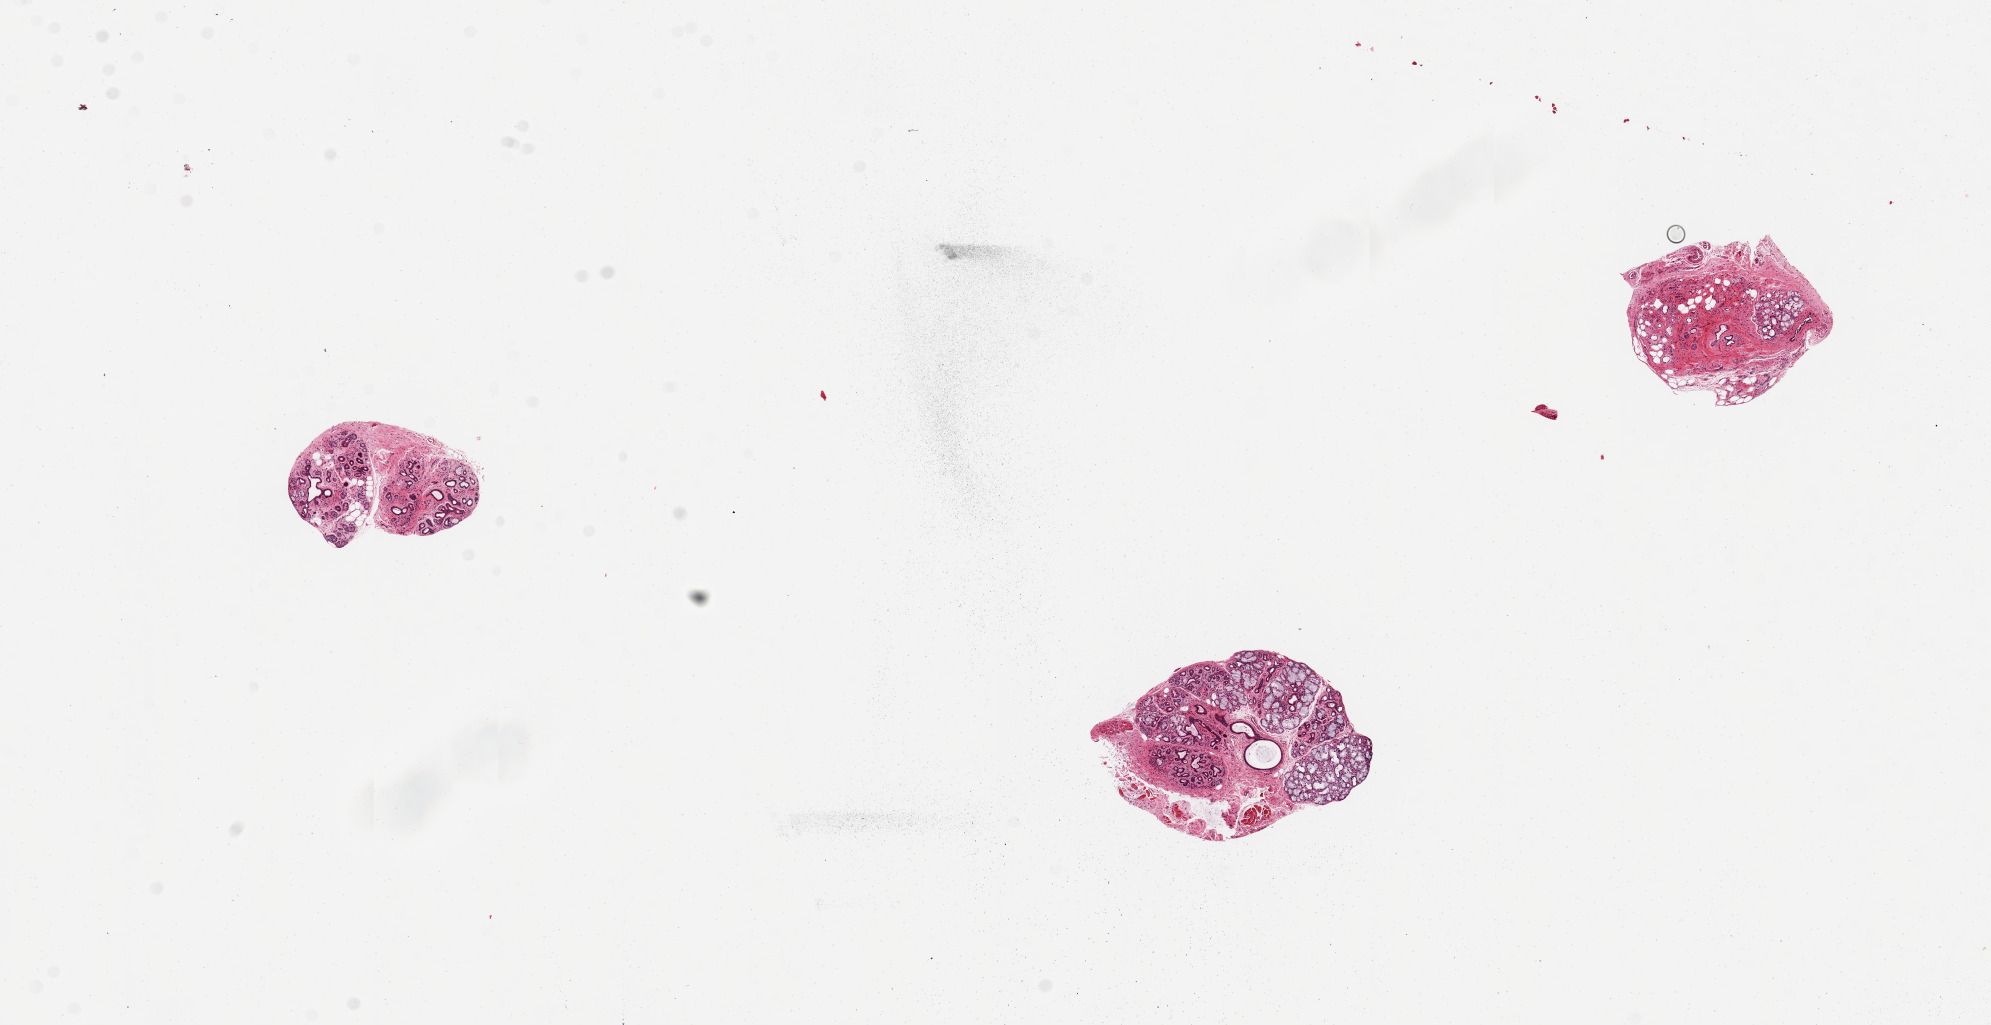
Whole-slide image, H&E stain, brightfield — low-resolution overview of the scanned area, about 15.8 x 8.1 mm. PAXgene-fixed paraffin-embedded (PFPE) section. Target tissue: minor salivary gland. Tissue donor sample. Donor: female.
- reviewer comment on this tissue sample: 3 pieces, ~70% gland parenchyma rest stroma/connective tissue; Good specimens